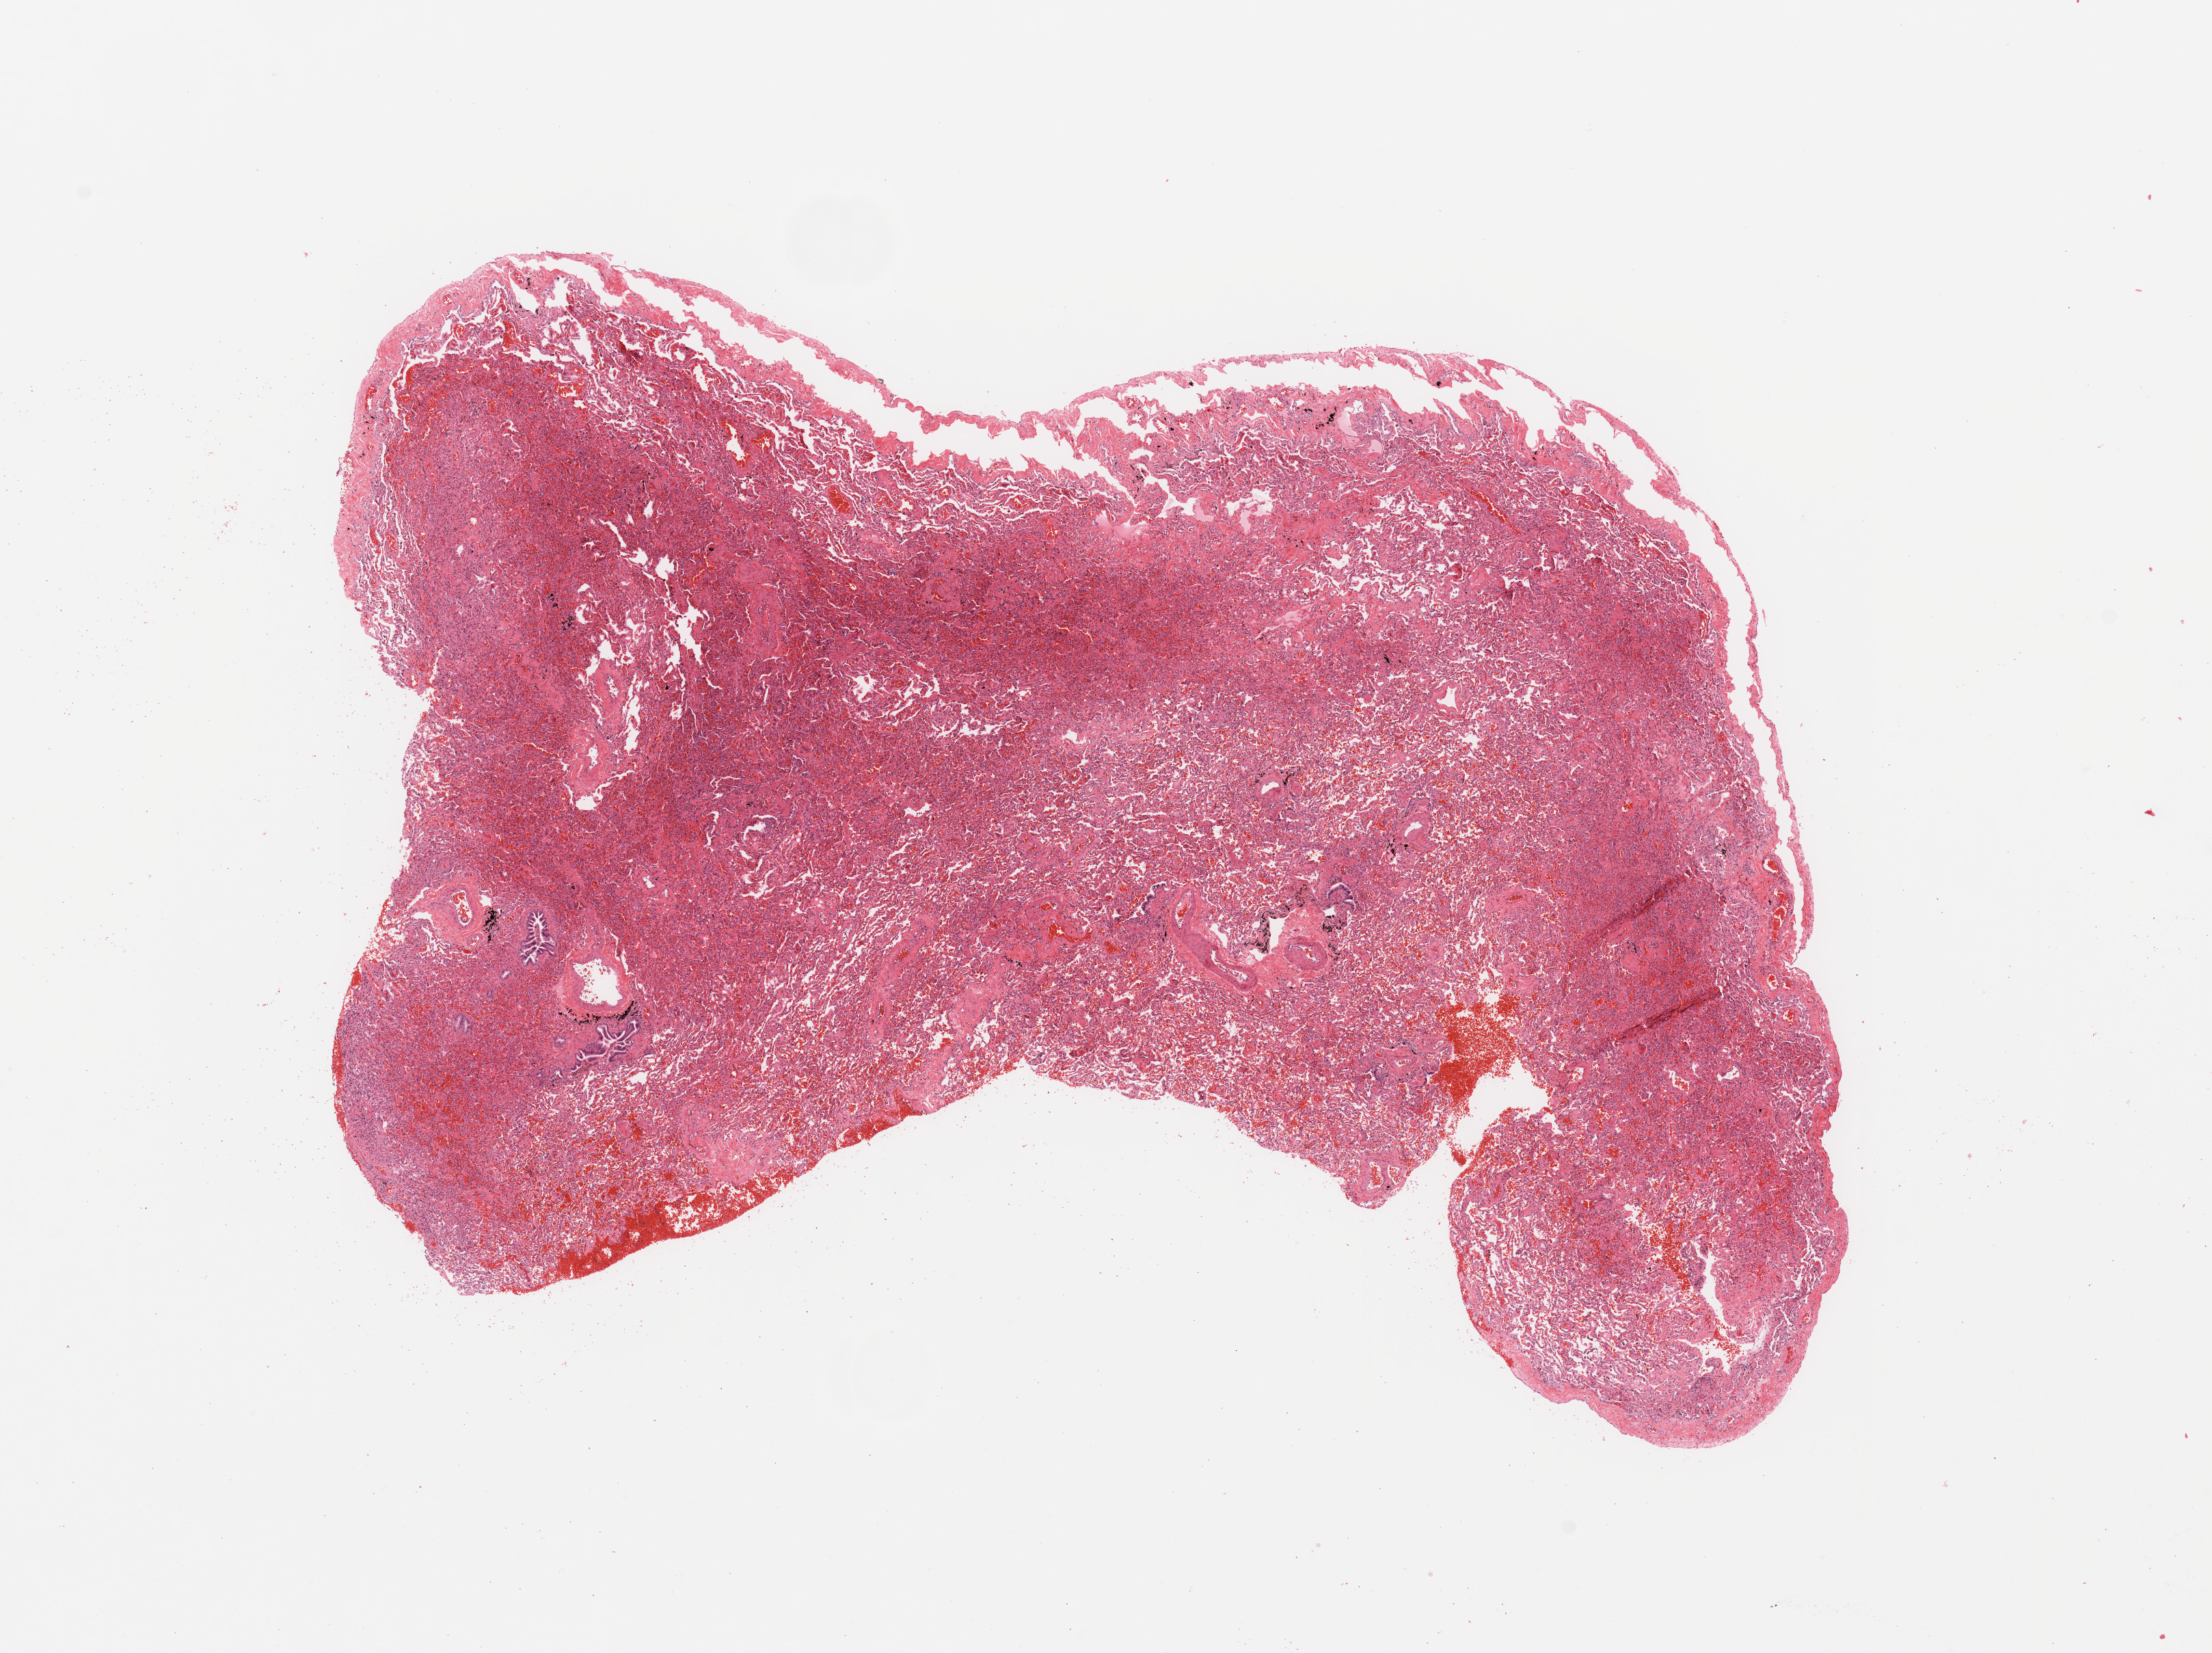
Whole-slide histology image, Hematoxylin and eosin (H&E) stained — low-resolution overview of the scanned area, about 12.8 x 9.6 mm (acquisition: 20x scan). Normal (non-tumour) tissue sample, sampled site: lung. Female, 44 y/o.
This section: normal (non-tumour) tissue from the same patient. Patient diagnosis: Adenocarcinoma, NOS.